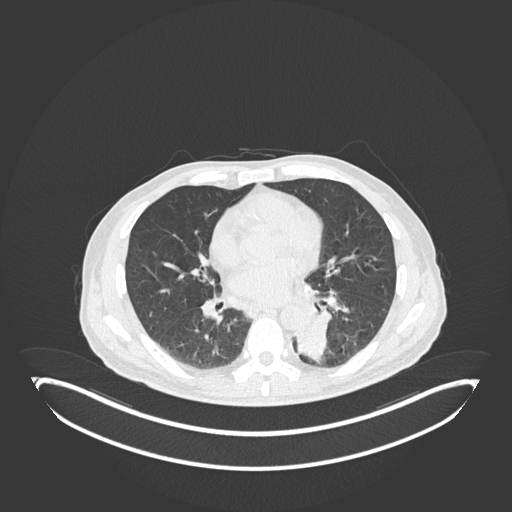
Chest CT, one axial slice; position 87 of 251 along the scan axis; 120 kVp; lung window (W 1500 / L -600 HU); 1 mm slice thickness; 512 × 512 image matrix, field of view 500 × 500 mm. Male patient, age 72 years. From the clinical record (not read from this slice): clinical TNM (as recorded): T2b N0 M1.
Outlined on this slice (bounding box drawn by a radiologist):
- lung tumour (recorded histology: adenocarcinoma): box from (x=293, y=311) to (x=335, y=364) px